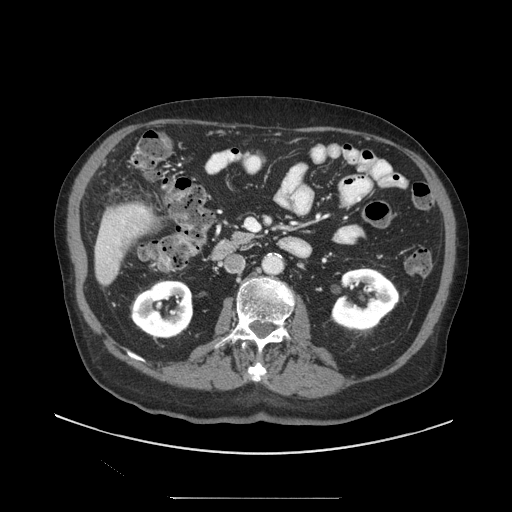
Contrast-enhanced abdominal CT (liver protocol), one axial slice. Slice 32 of 97 in the series (ordered by position). Reconstruction kernel STANDARD. 140 kVp. Soft-tissue window (W 400 / L 40 HU). 512 × 512 image matrix, field of view 450 × 450 mm. Case-level facts recorded for this patient, not image findings: diagnosis: hepatocellular carcinoma (patient treated with transarterial chemoembolisation; whether this scan precedes or follows treatment is not stated here); TNM stage (as recorded): Stage-IIIC; Child-Pugh class: A; tumour differentiation: well differentiated; tumour nodularity: uninodular.
Structures marked on this image (semi-automatic segmentation, software-assisted and operator-edited):
- liver parenchyma outside the tumour (the mass and vessels are separate outlines, so this box may not span the whole liver): box from (x=94, y=202) to (x=154, y=286) px
- liver vessels: (x=121, y=209)–(x=144, y=224)